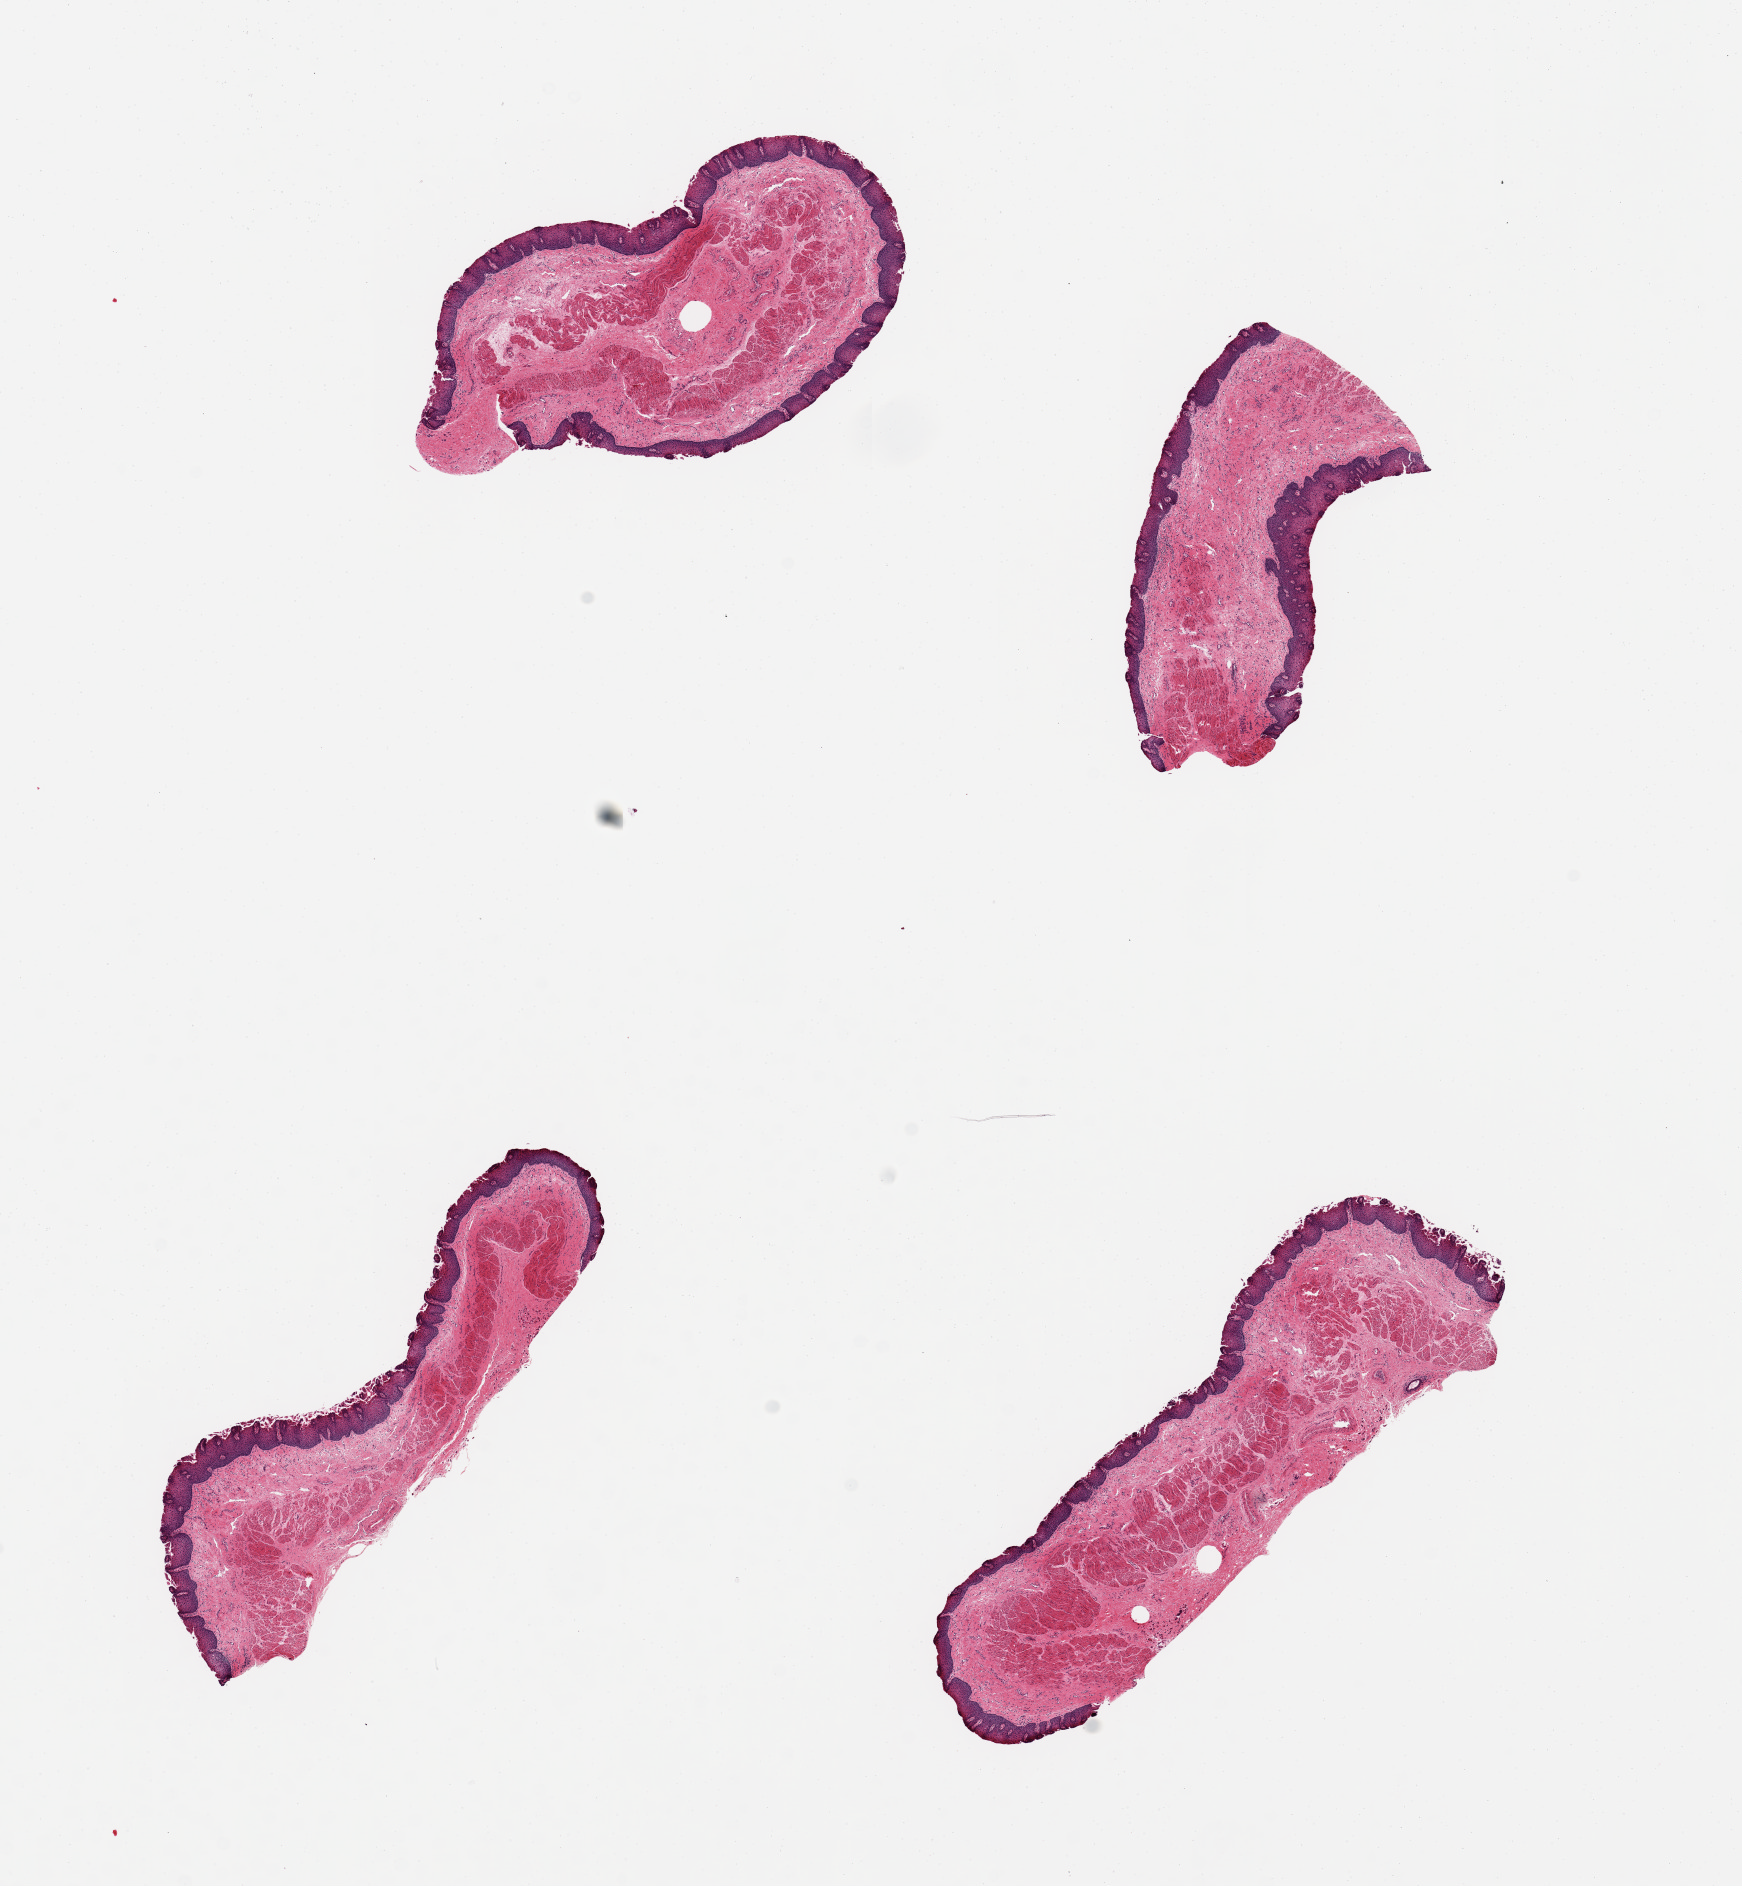
Haematoxylin and eosin whole-slide image — a low-resolution overview of the entire scanned area, about 13.8 x 14.9 mm; PAXgene-fixed paraffin-embedded (PFPE) section; sampled site (target tissue): esophageal mucous membrane; tissue donor sample.
Review note (as recorded): 4 pieces.